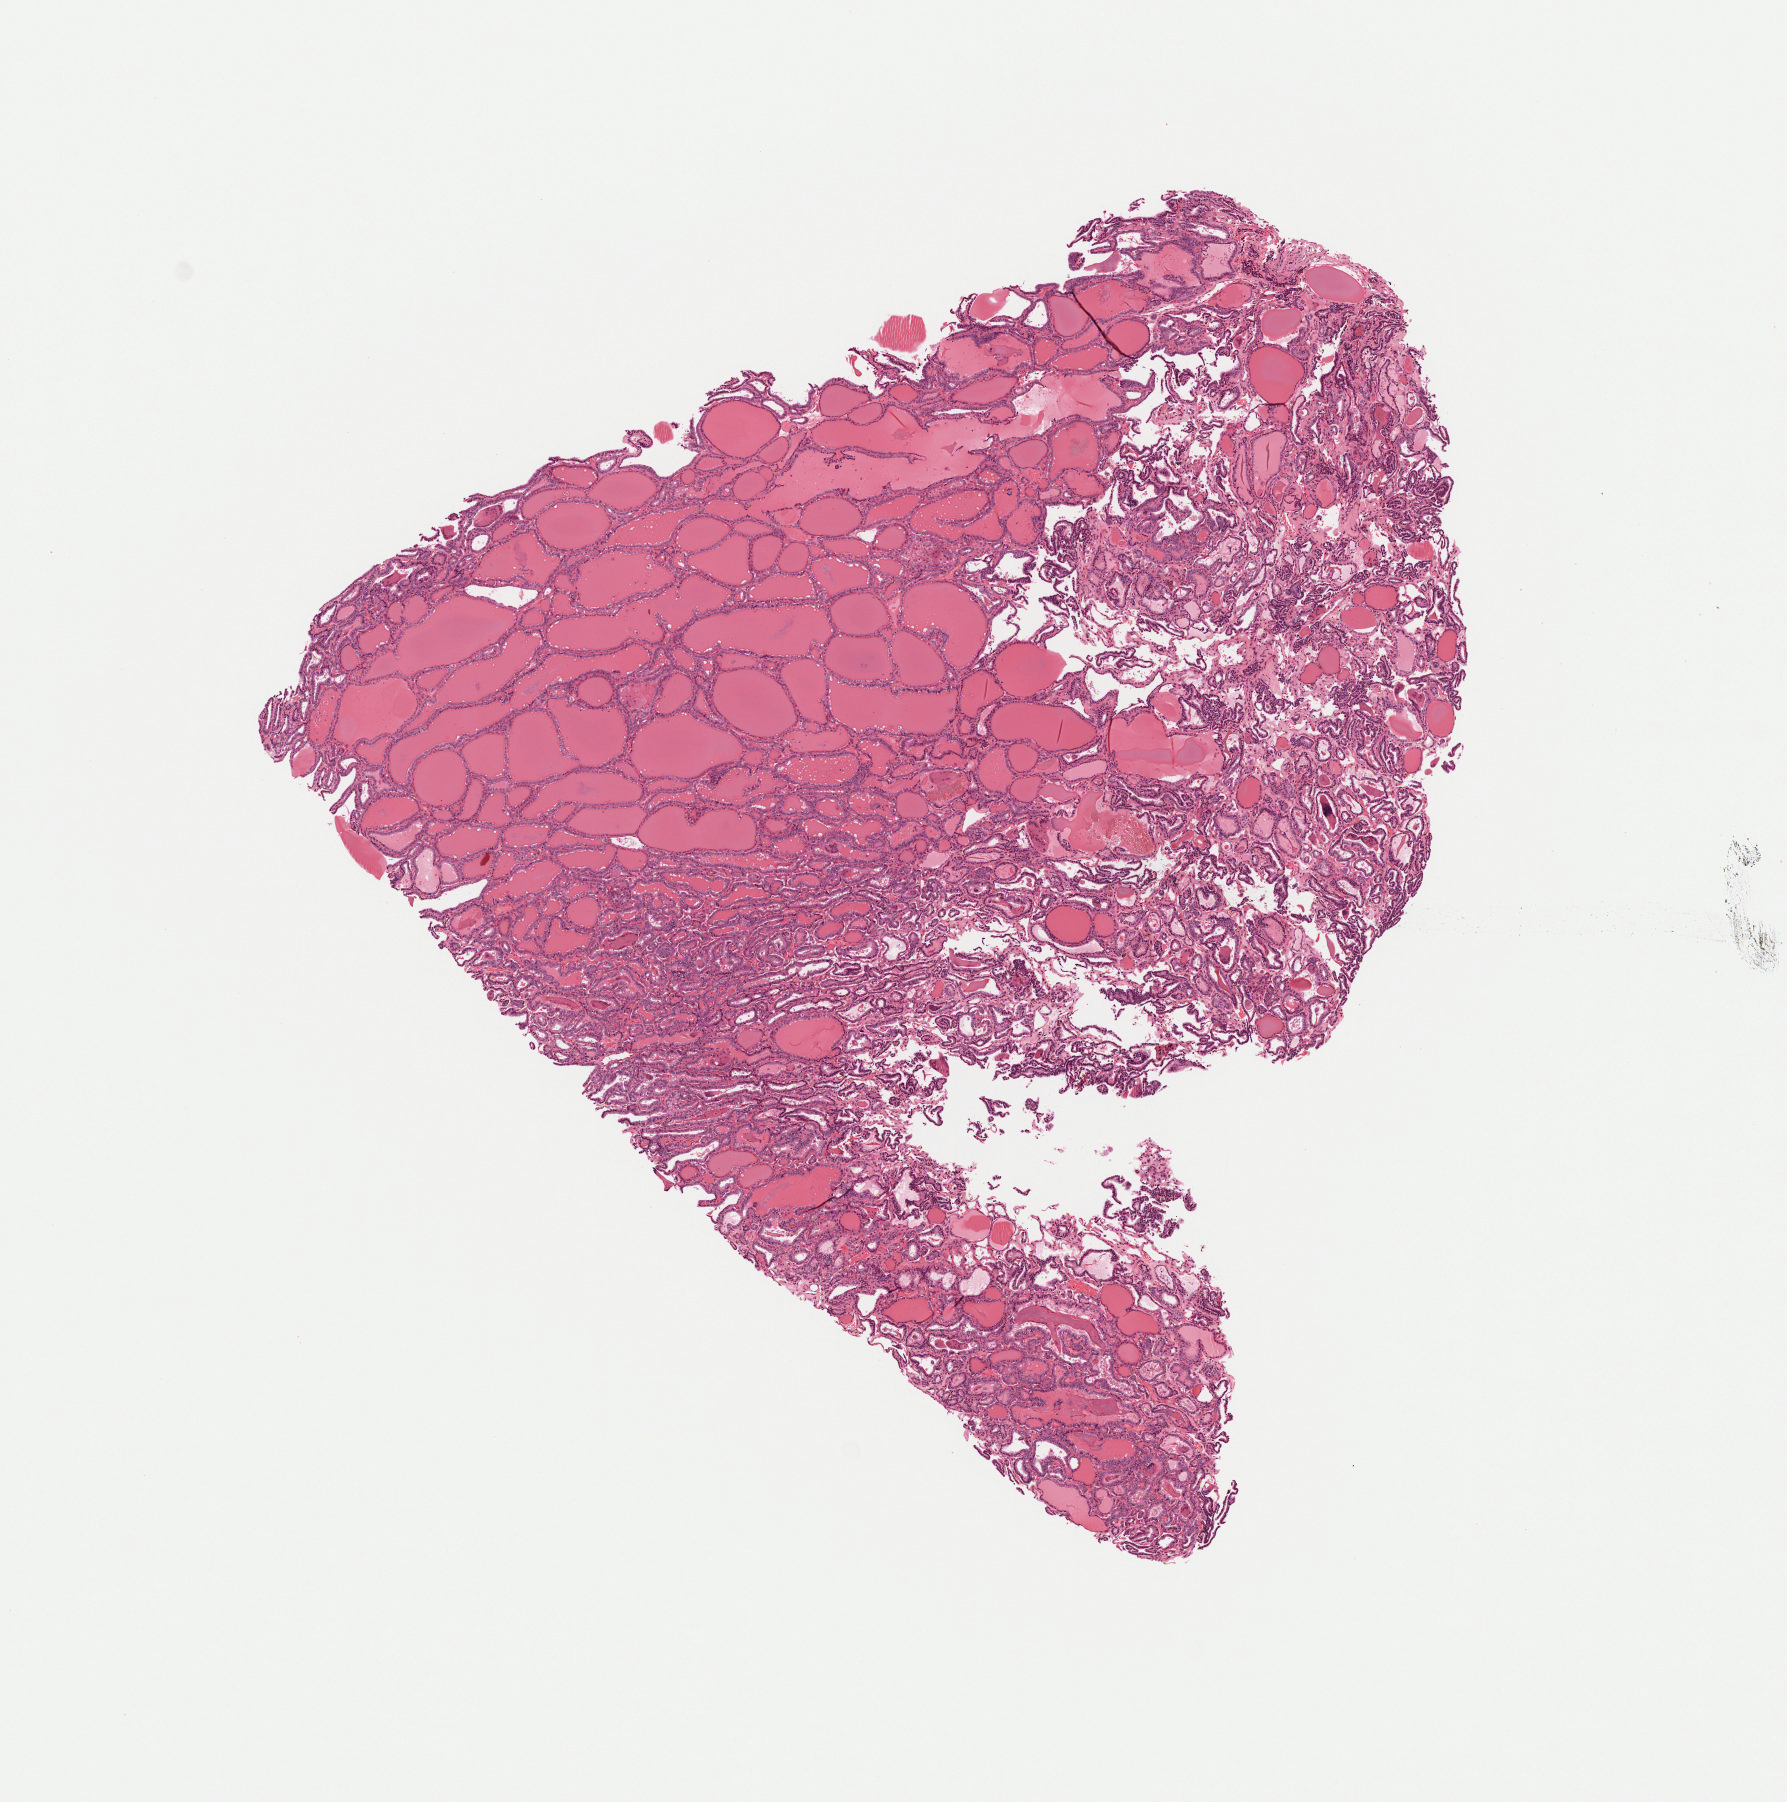
Digitized H&E-stained tissue section (whole slide) — shown as a low-resolution overview of the whole scanned area (about 7.2 x 7.3 mm, from a 40x scan), formalin-fixed paraffin-embedded (FFPE) diagnostic section, primary tumour sample from the thyroid. Female patient; age at initial diagnosis 64 years.
Diagnosis: Papillary adenocarcinoma, NOS.